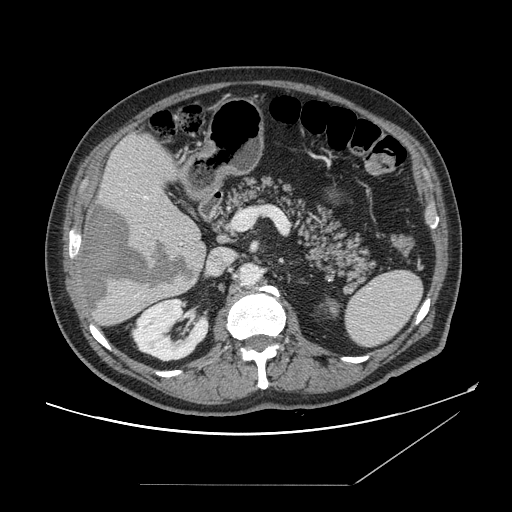
Contrast-enhanced abdominal CT, one axial slice. Position 81 of 166 along the scan axis. 120 kVp. Intravenous contrast given. Soft-tissue window (W 400 / L 40 HU). 2.5 mm slice thickness. 512 × 512 image matrix. Male patient, age 80 years. Case-level facts recorded for this patient, not image findings: diagnosis: colorectal cancer liver metastases, imaged before liver resection; multiple liver metastases: no; largest metastasis: 2.2 cm.
Outlined on this slice (outlined manually by an expert reader):
- hepatic veins: bounding box (x1, y1, x2, y2) in pixels: (146, 197, 148, 200)
- liver: (78, 133, 207, 327)
- planned liver remnant (the part of the liver to remain after resection): (102, 133, 201, 236)
- liver metastasis: (83, 205, 194, 311)